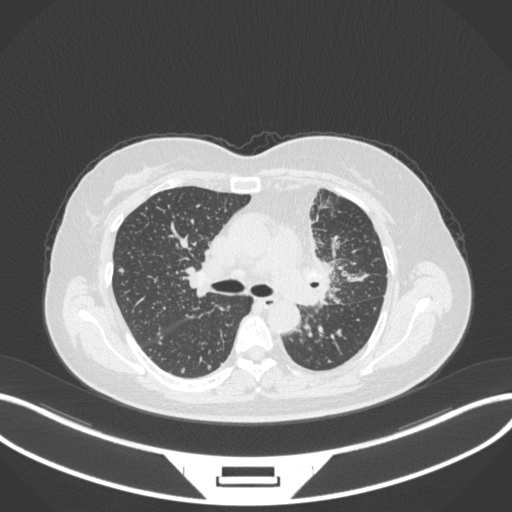
Chest CT, one axial slice. Position 210 of 348 along the scan axis. Lung window (W 1500 / L -600 HU). 512 × 512 image matrix. Female patient, age 49 years. From the clinical record (not read from this slice): clinical TNM (as recorded): T1c N0 M1.
Structures marked on this image (rectangle marked by the reading radiologist):
- lung tumour (recorded histology: adenocarcinoma): box from (x=296, y=253) to (x=340, y=307) px